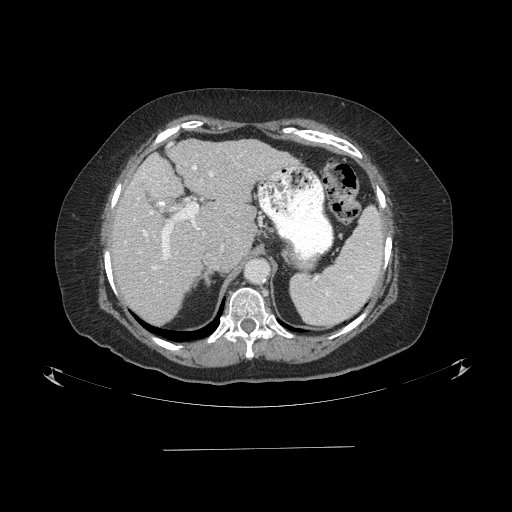
Contrast-enhanced abdominal CT (liver protocol), one axial slice. Position 58 of 103 along the scan axis. Reconstruction kernel STANDARD. 120 kVp. One of 2 acquisitions stored at this slice position. Soft-tissue window (W 400 / L 40 HU). 2.5 mm slice thickness. 512 × 512 image matrix, field of view 500 × 500 mm. From the clinical record (not read from this slice): diagnosis: hepatocellular carcinoma (patient treated with transarterial chemoembolisation; whether this scan precedes or follows treatment is not stated here); TNM stage (as recorded): Stage-IIIA; Child-Pugh class: A; tumour differentiation: poorly differentiated; tumour nodularity: multinodular.
Annotated regions visible in this slice (semi-automatically segmented with operator editing):
- abdominal aorta: bounding box <246,260,268,282> (left, top, right, bottom; pixels)
- liver parenchyma outside the tumour (the mass and vessels are separate outlines, so this box may not span the whole liver): <112,138,294,324>
- liver vessels: <140,145,213,270>